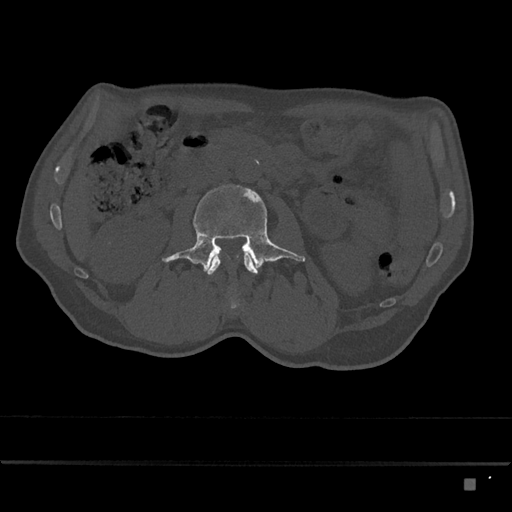
CT including the spine, one axial slice; slice 426 of 797 in the series (ordered by position); reconstruction kernel Br40s/3; 120 kVp; bone window (W 1800 / L 400 HU); 0.5 mm slice thickness; 512 × 512 image matrix, field of view 390 × 390 mm. Patient: male, 72 years. From the clinical record (not read from this slice): primary cancer: prostate.
Structures marked on this image (semi-automatic segmentation, software-assisted and operator-edited):
- L2 vertebra: bounding box (x1, y1, x2, y2) in pixels: (203, 253, 258, 275)
- L3 vertebra: (162, 184, 306, 294)